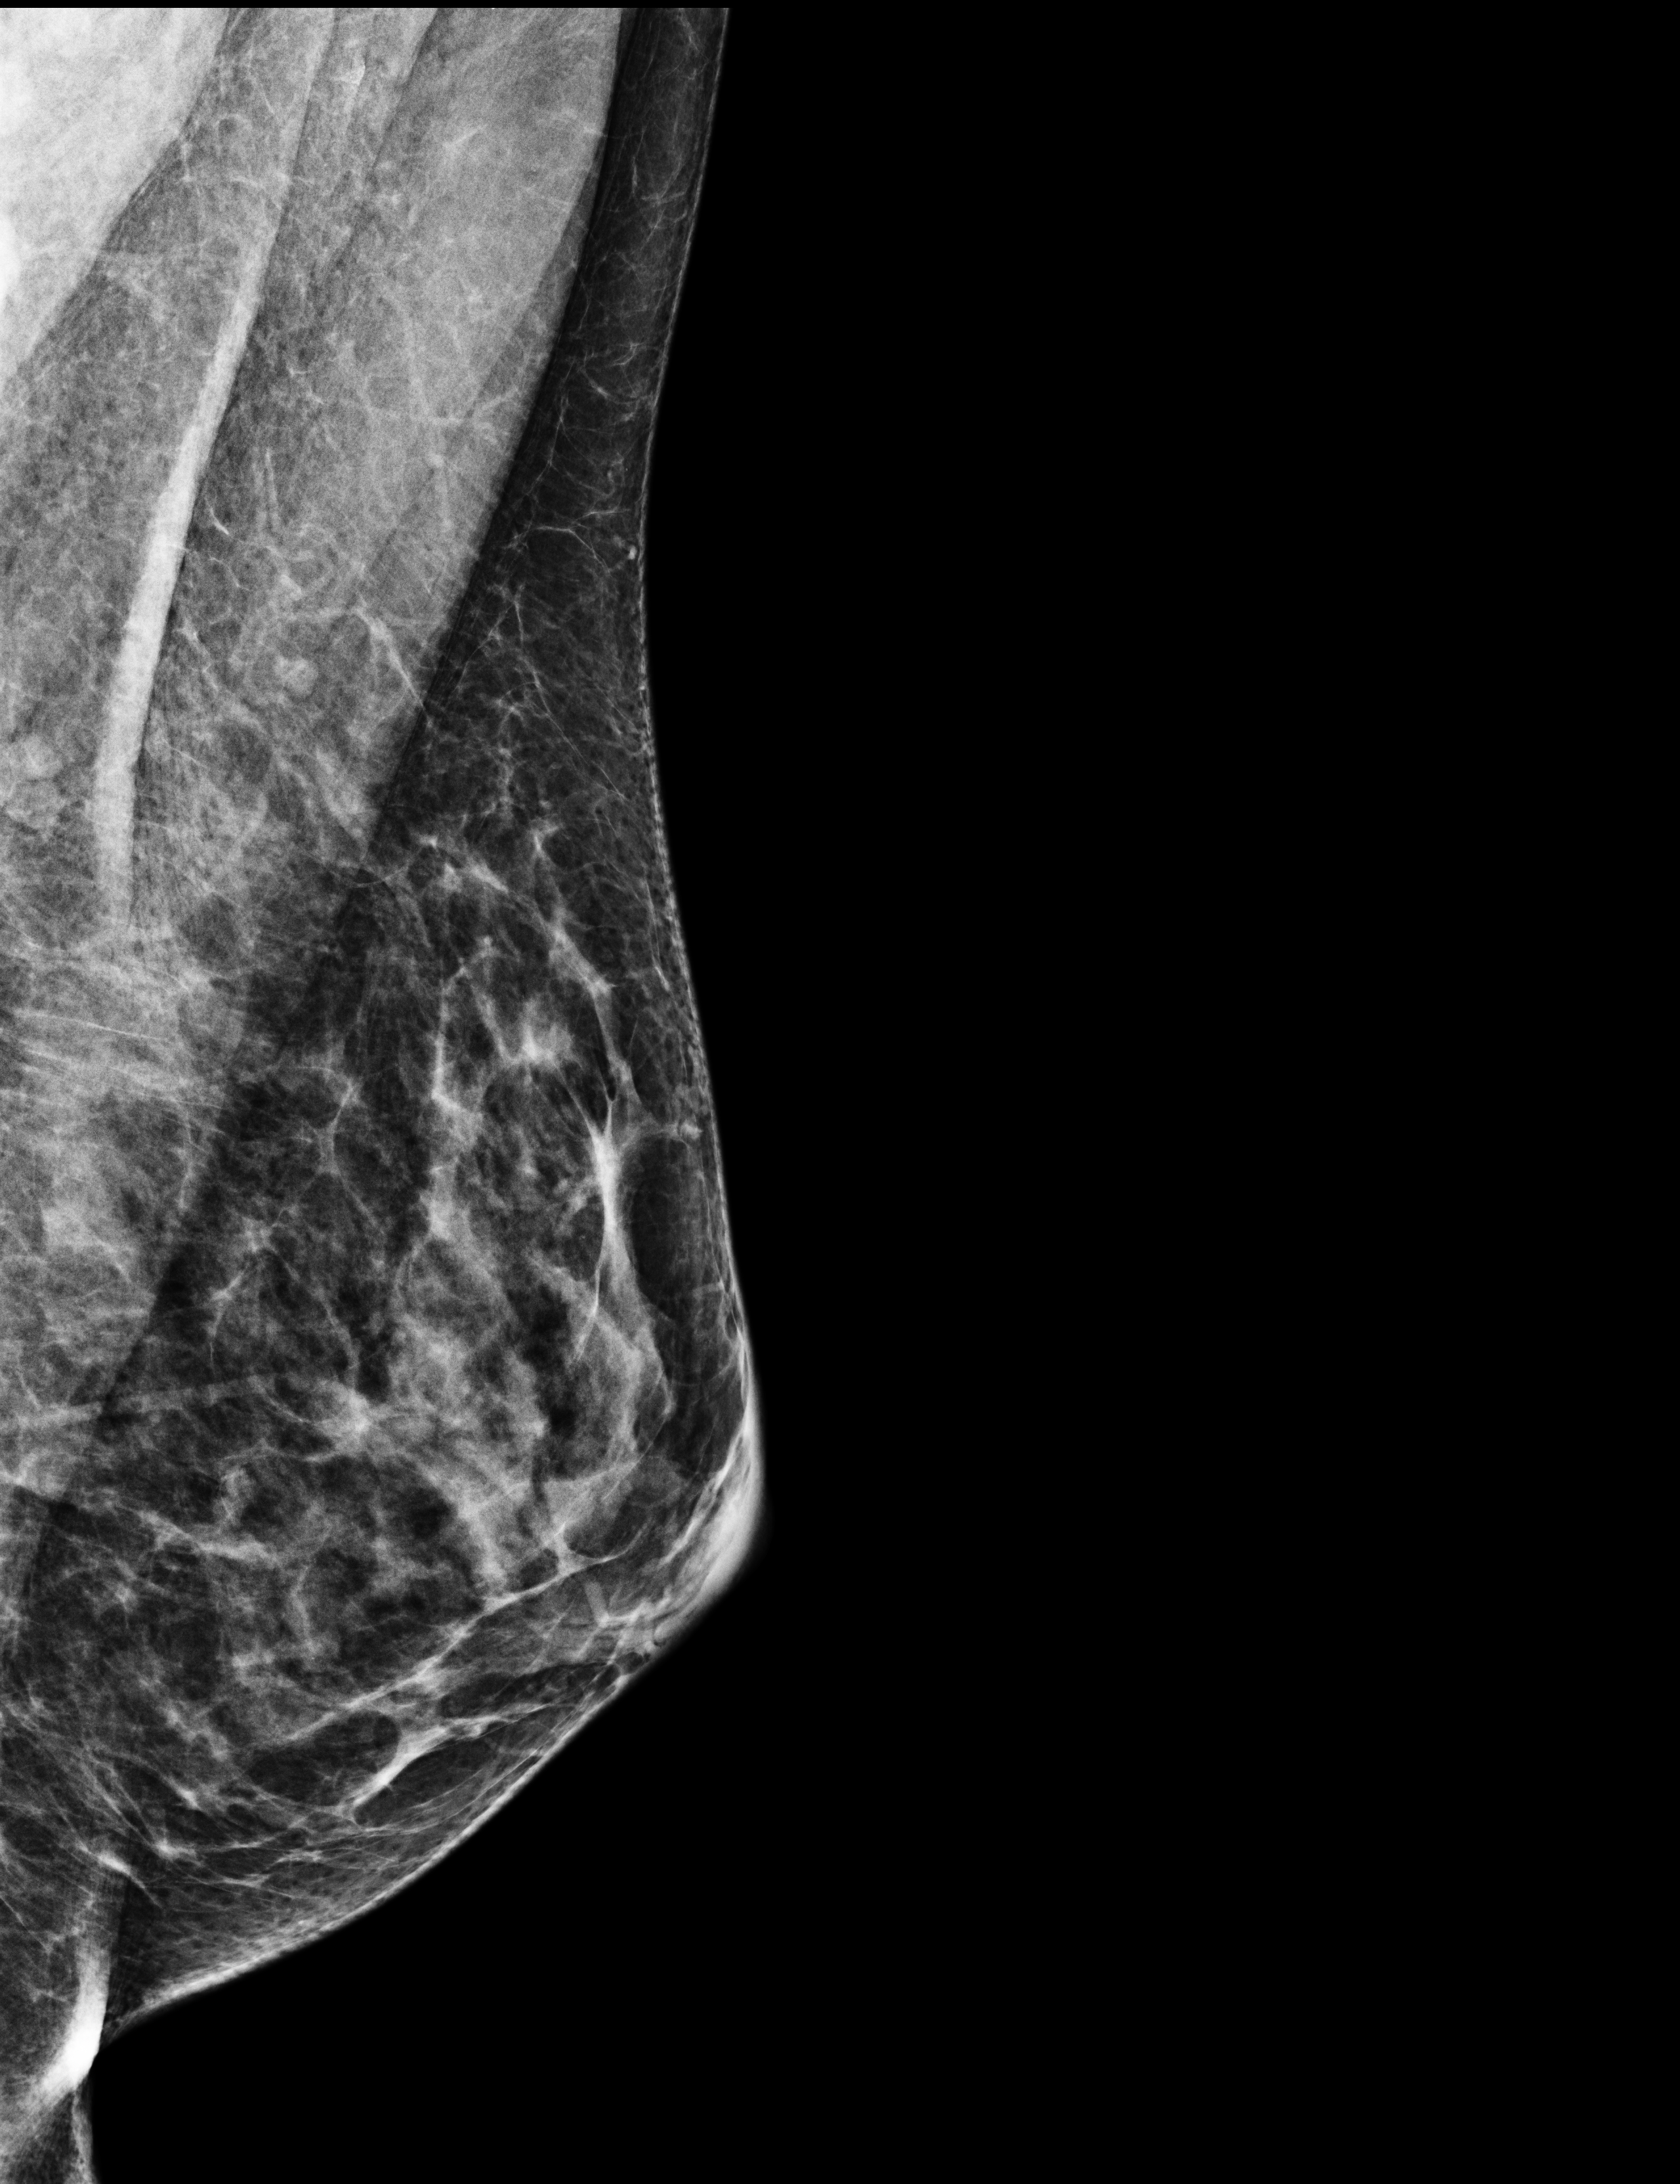
Annual screening mammography examination.
Image type: full-field digital mammogram. Breast: left. Projection: mediolateral oblique (MLO) view.